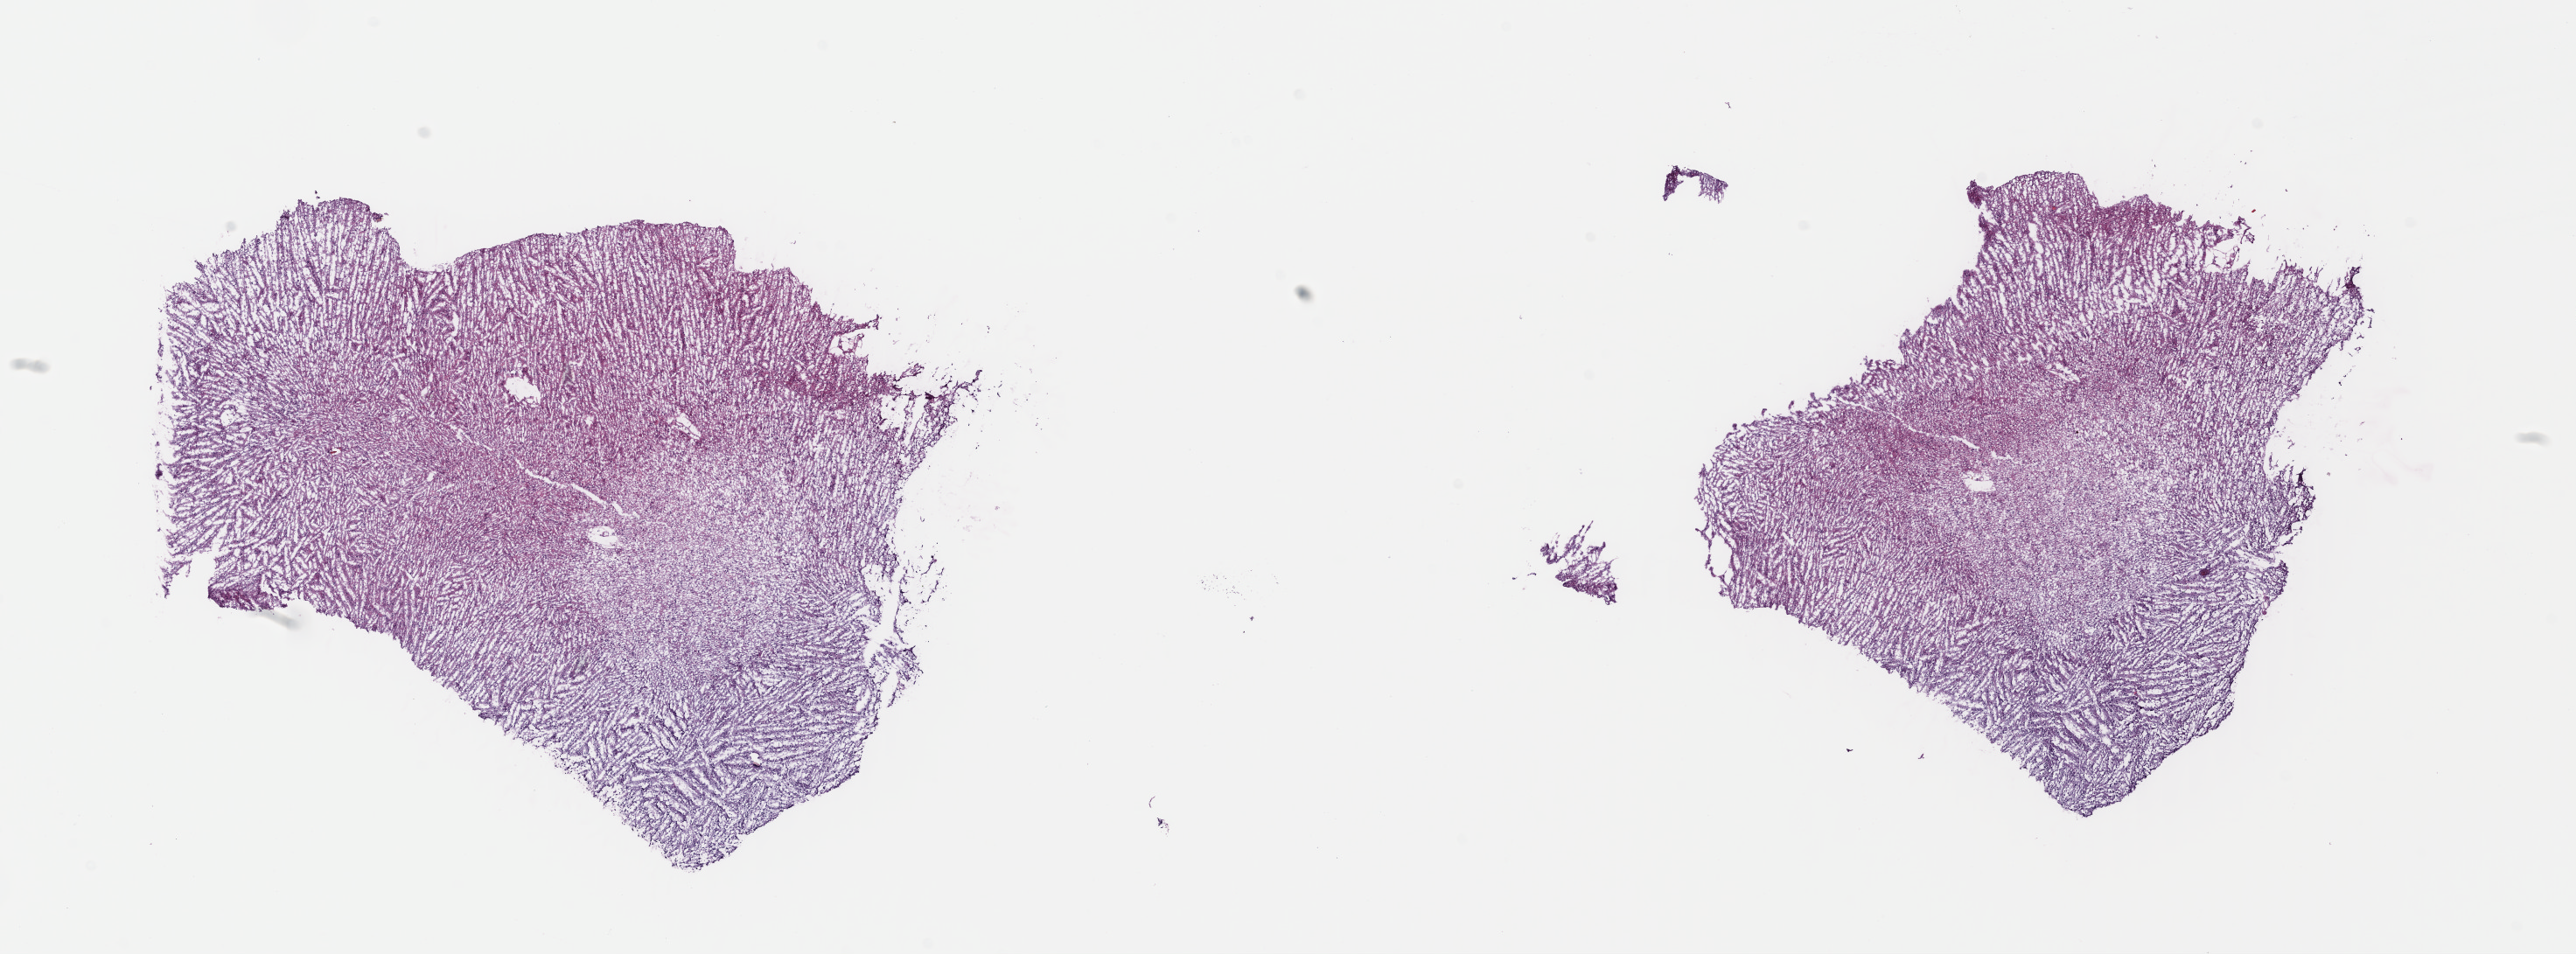
H&E-stained whole-slide image — a low-resolution overview of the entire scanned area, about 23.1 x 8.6 mm (from a 40x scan). Frozen section from the top of the tissue portion. Sample: primary tumour, brain. Patient: male, age at initial diagnosis 42 years. Histologic grade: G3 (poorly differentiated). Pathologist review of this section (percent, as recorded): tumour cells 40%, tumour nuclei 80%, normal cells 10%, stromal cells 50%, necrosis 0%. Infiltration values recorded for this section: lymphocyte infiltration 0%, monocyte infiltration 0%, neutrophil infiltration 0%.
Histologic diagnosis: Mixed glioma (cerebrum).